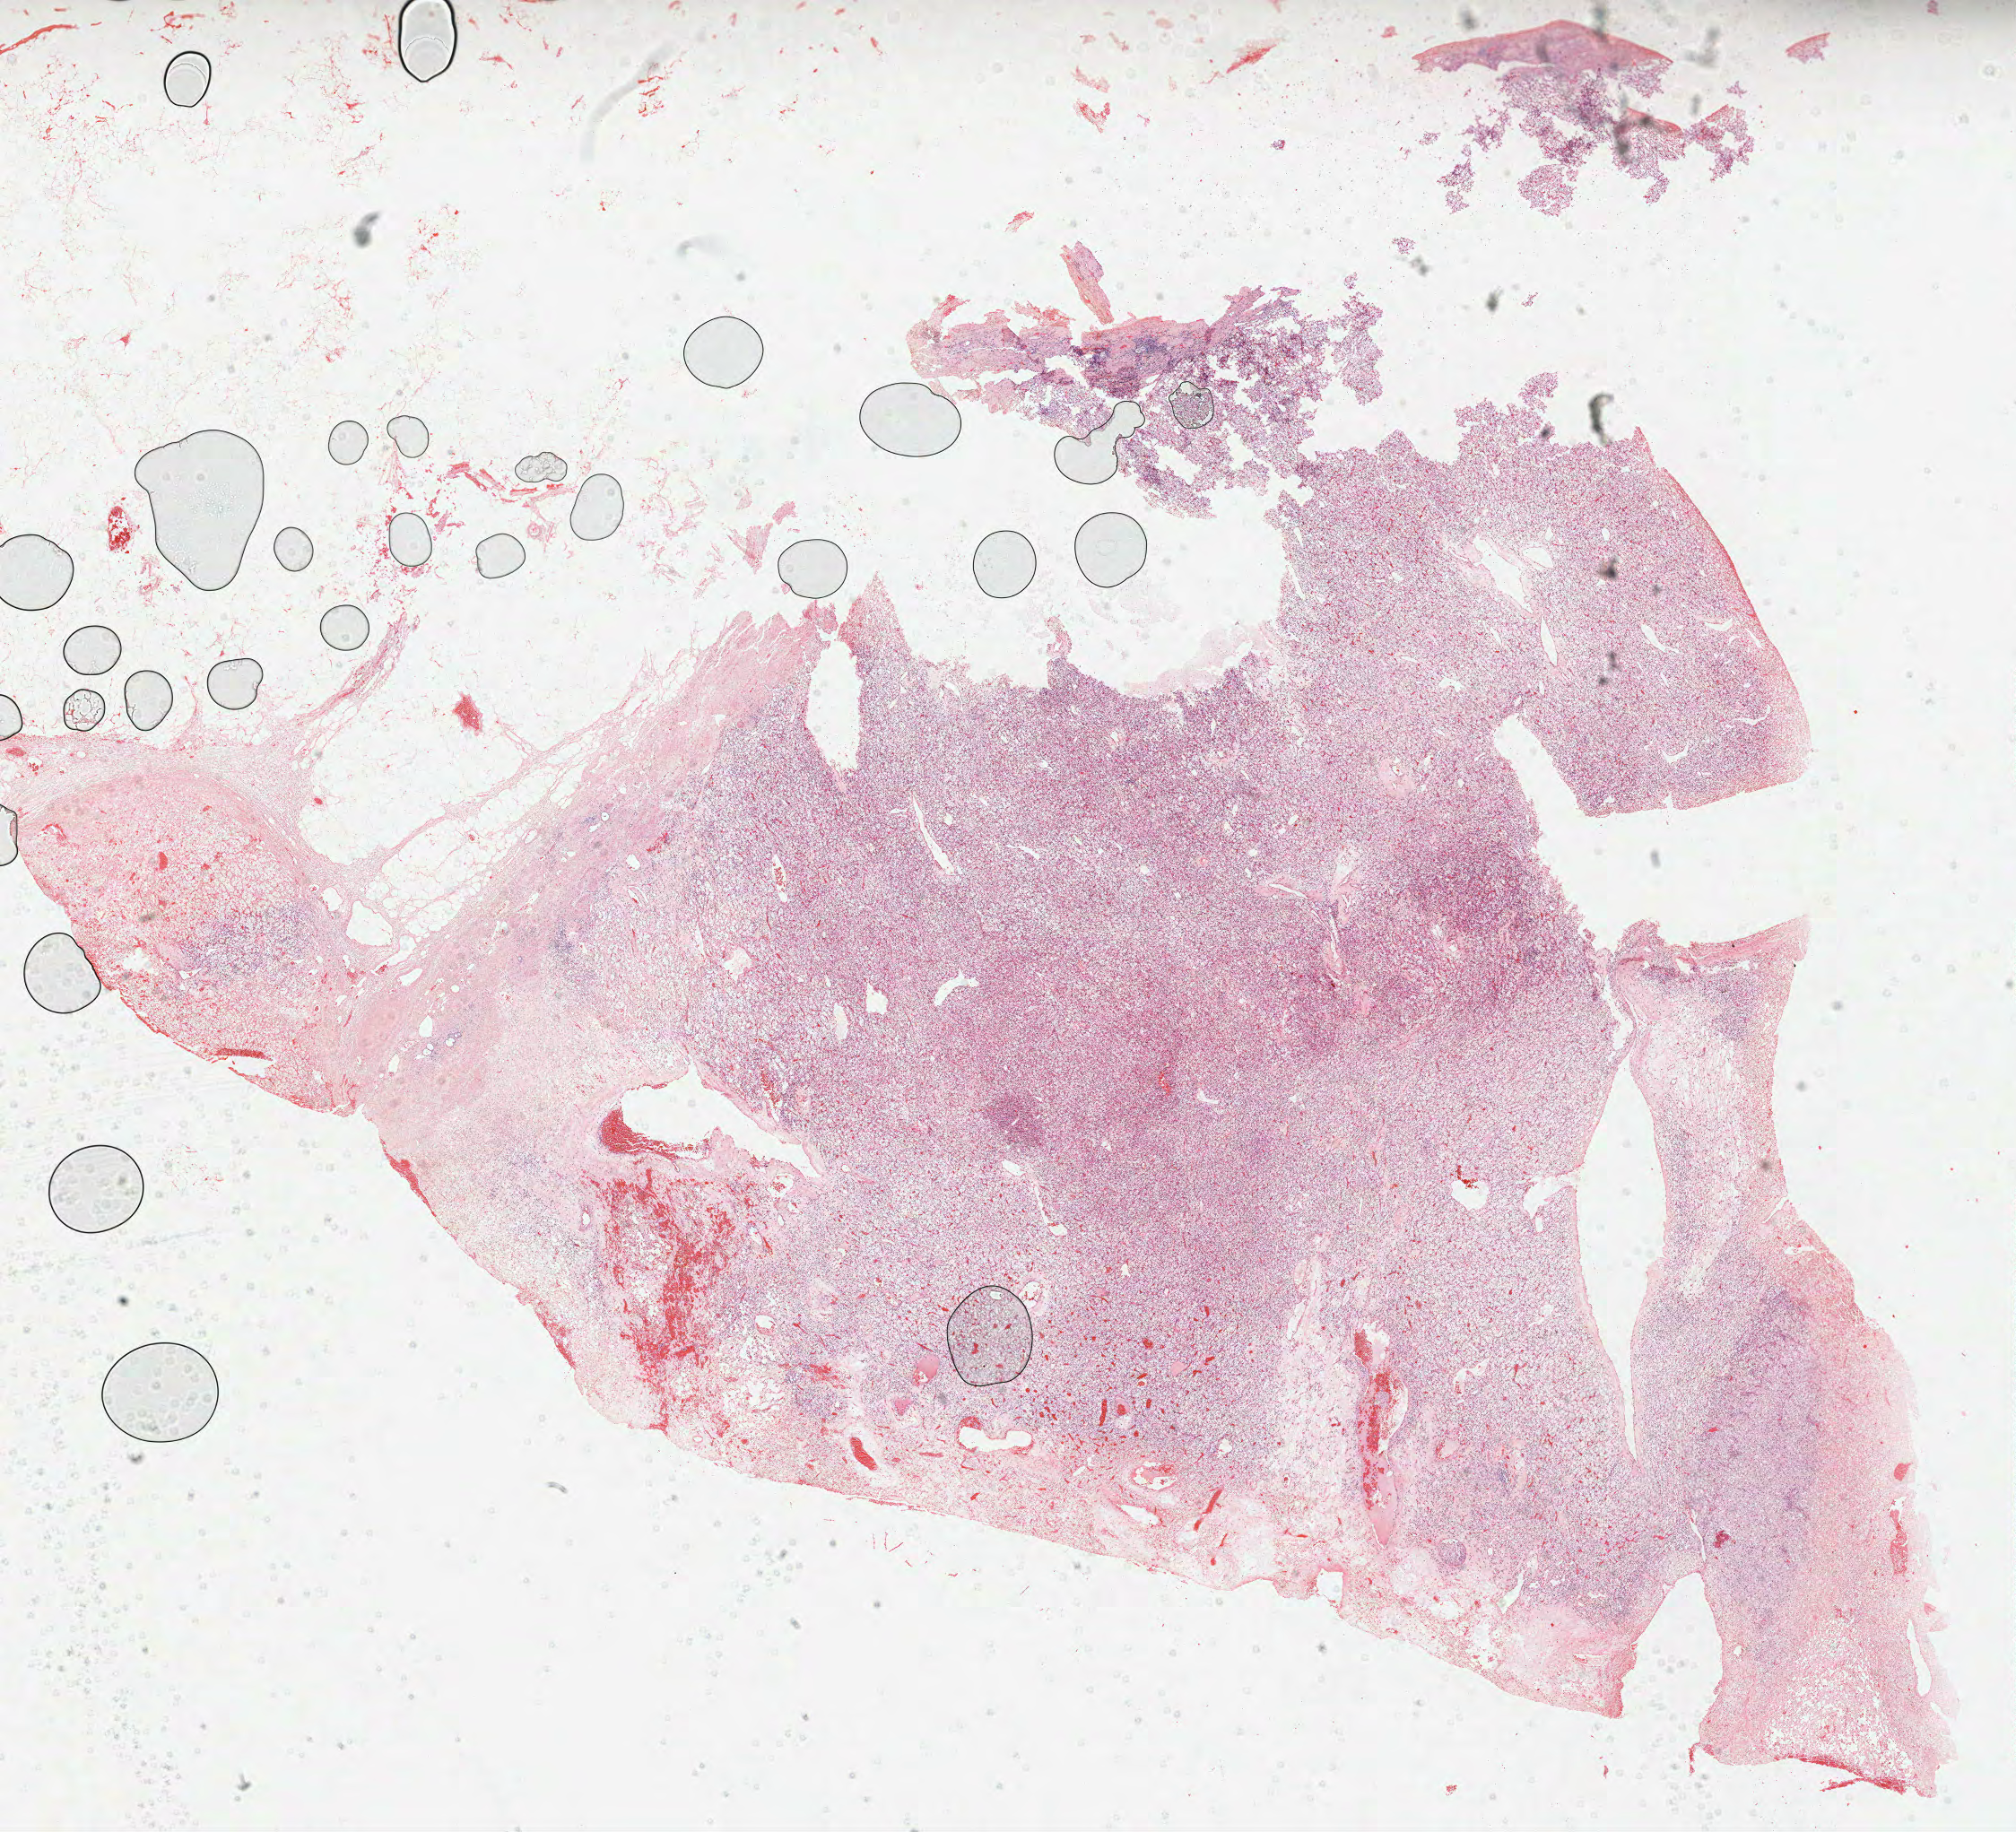
Whole-slide histology image, H&E — a low-resolution overview of the entire scanned area, about 18.1 x 16.5 mm (acquisition: 40x scan). Formalin-fixed paraffin-embedded (FFPE) diagnostic section. Sample: primary tumour, kidney. Patient: female, age at initial diagnosis 72 years. Histologic grade: GX (grade cannot be assessed).
Laterality: left. Pathologic diagnosis: Clear cell adenocarcinoma, NOS. AJCC pathologic stage: III. TNM: T3a N1 M0. Lymph nodes positive (case pathology): 1 of 1 examined.